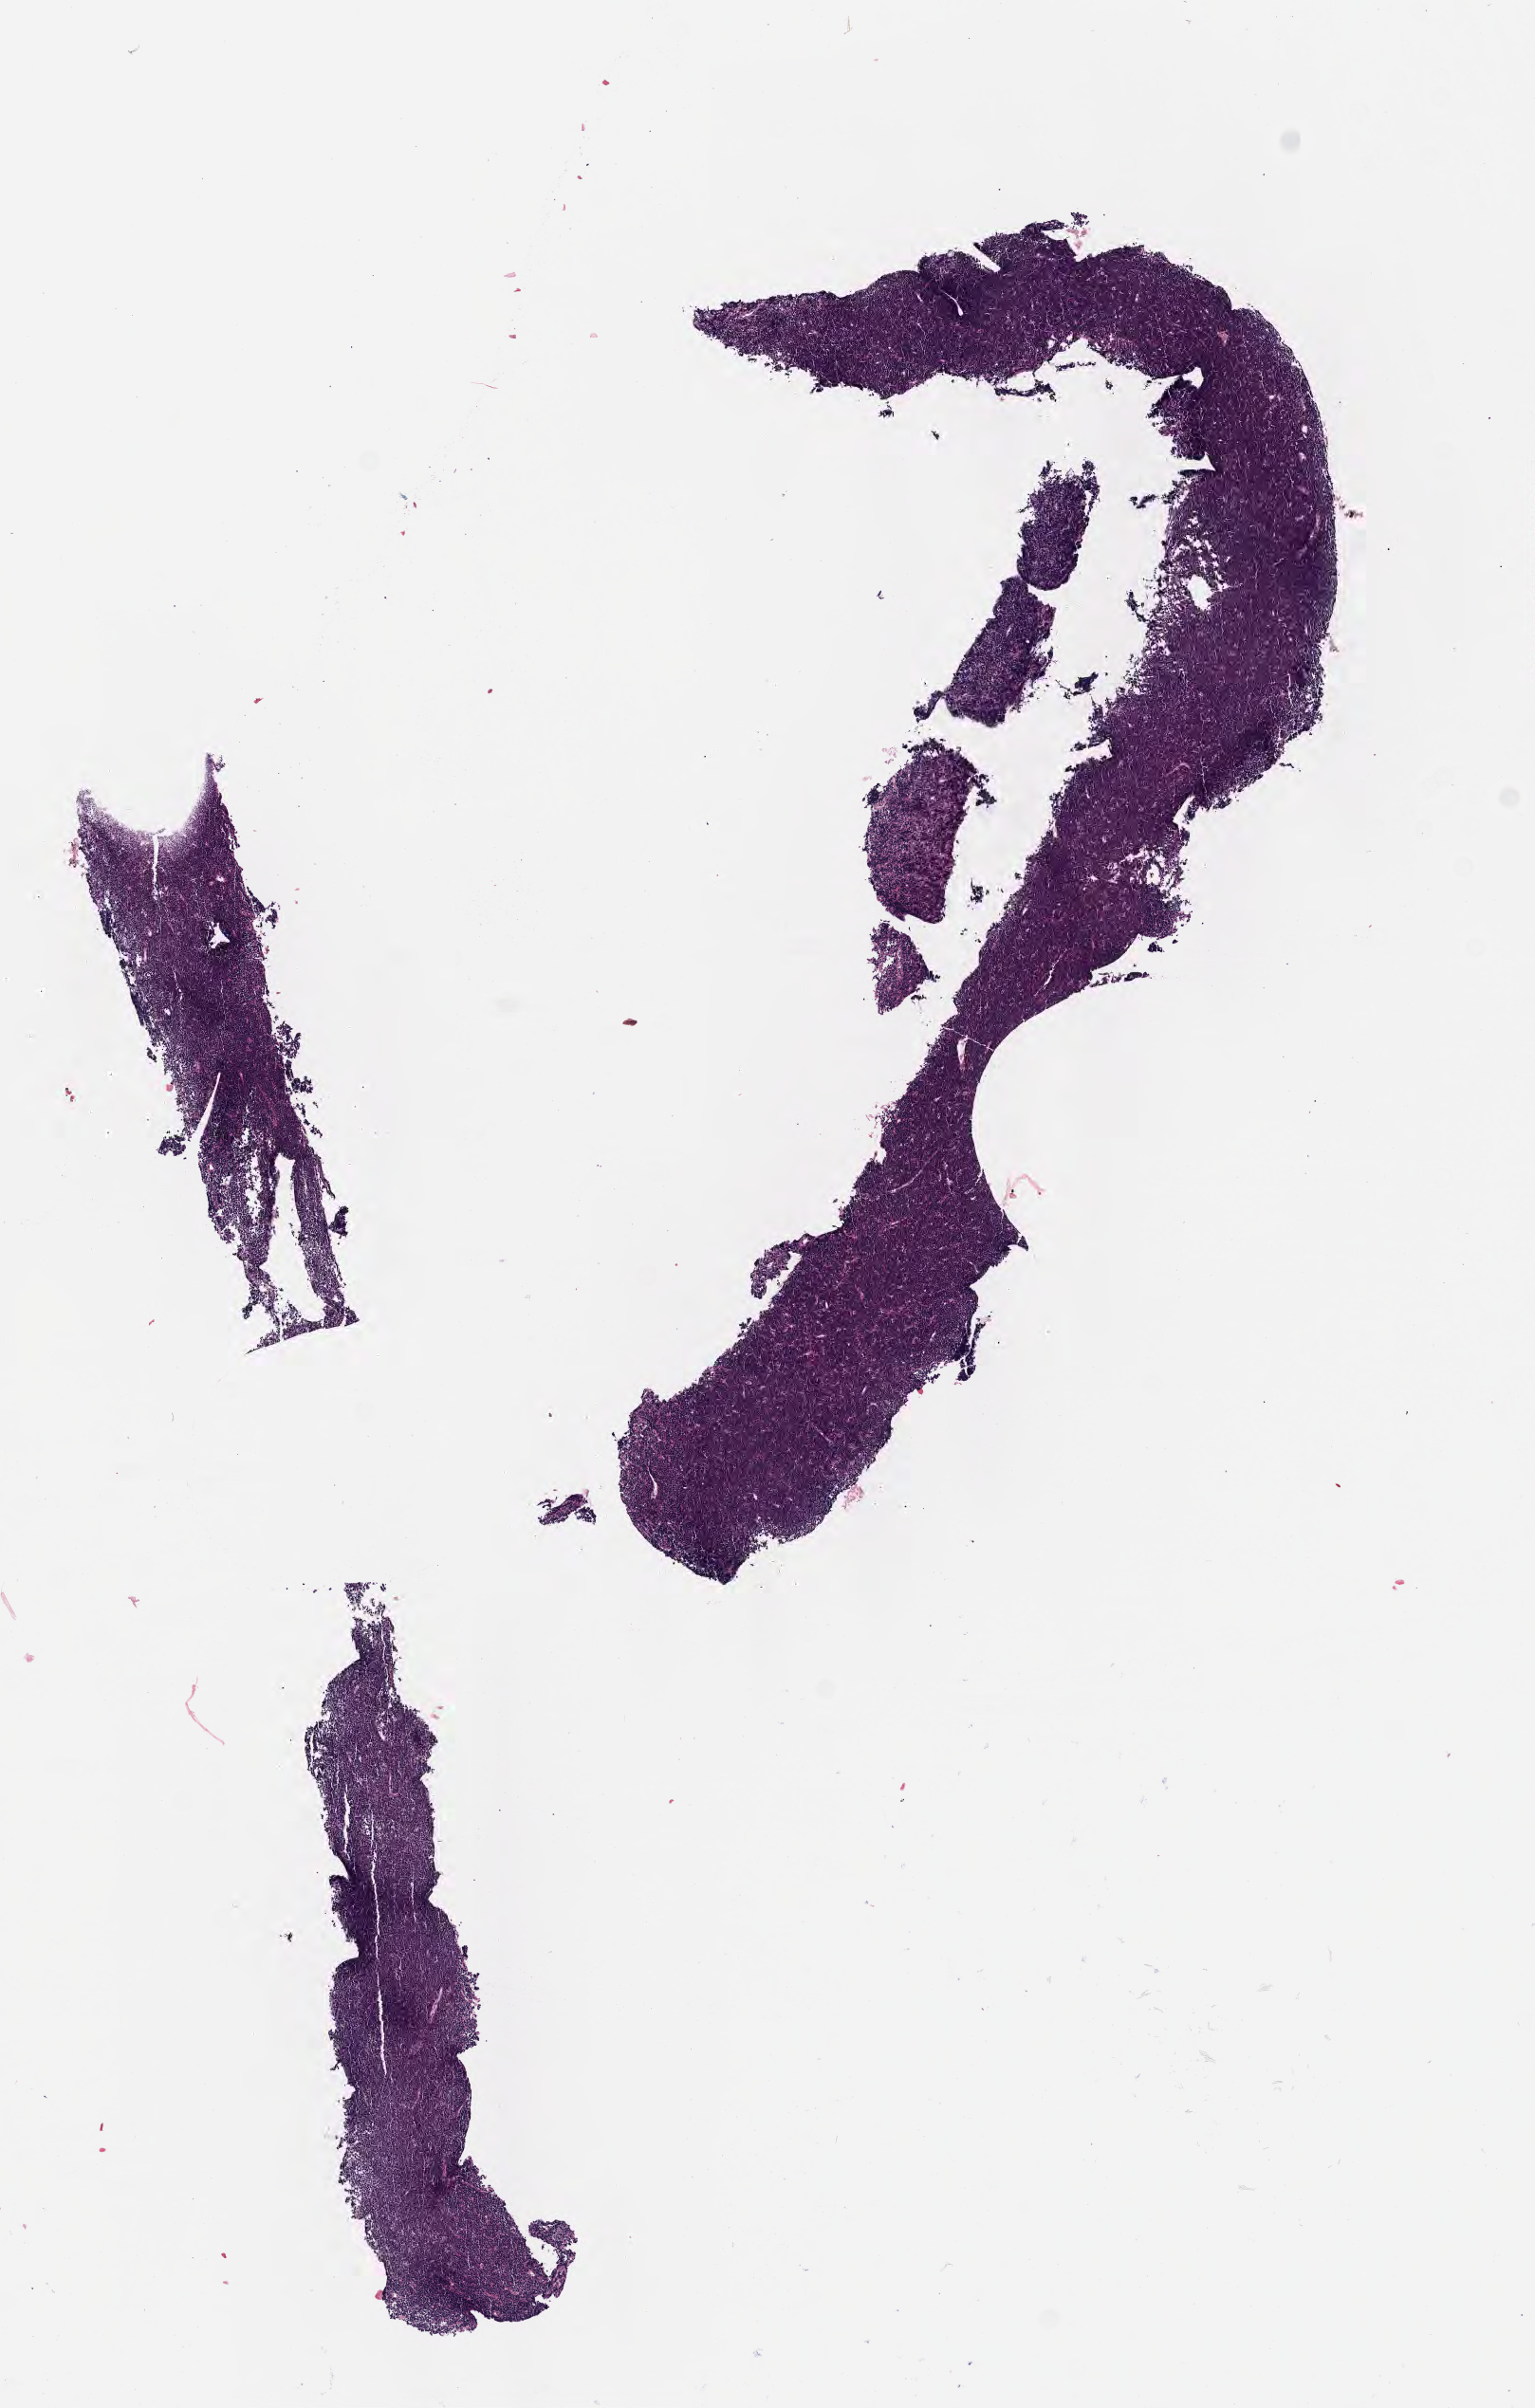
Digitized H&E-stained section, low-resolution overview of the scanned area, about 6.5 x 10.3 mm. Tumor tissue. Site: peritoneum. Female patient; age at initial diagnosis 7 years.
Diagnosis: Burkitt lymphoma, NOS.